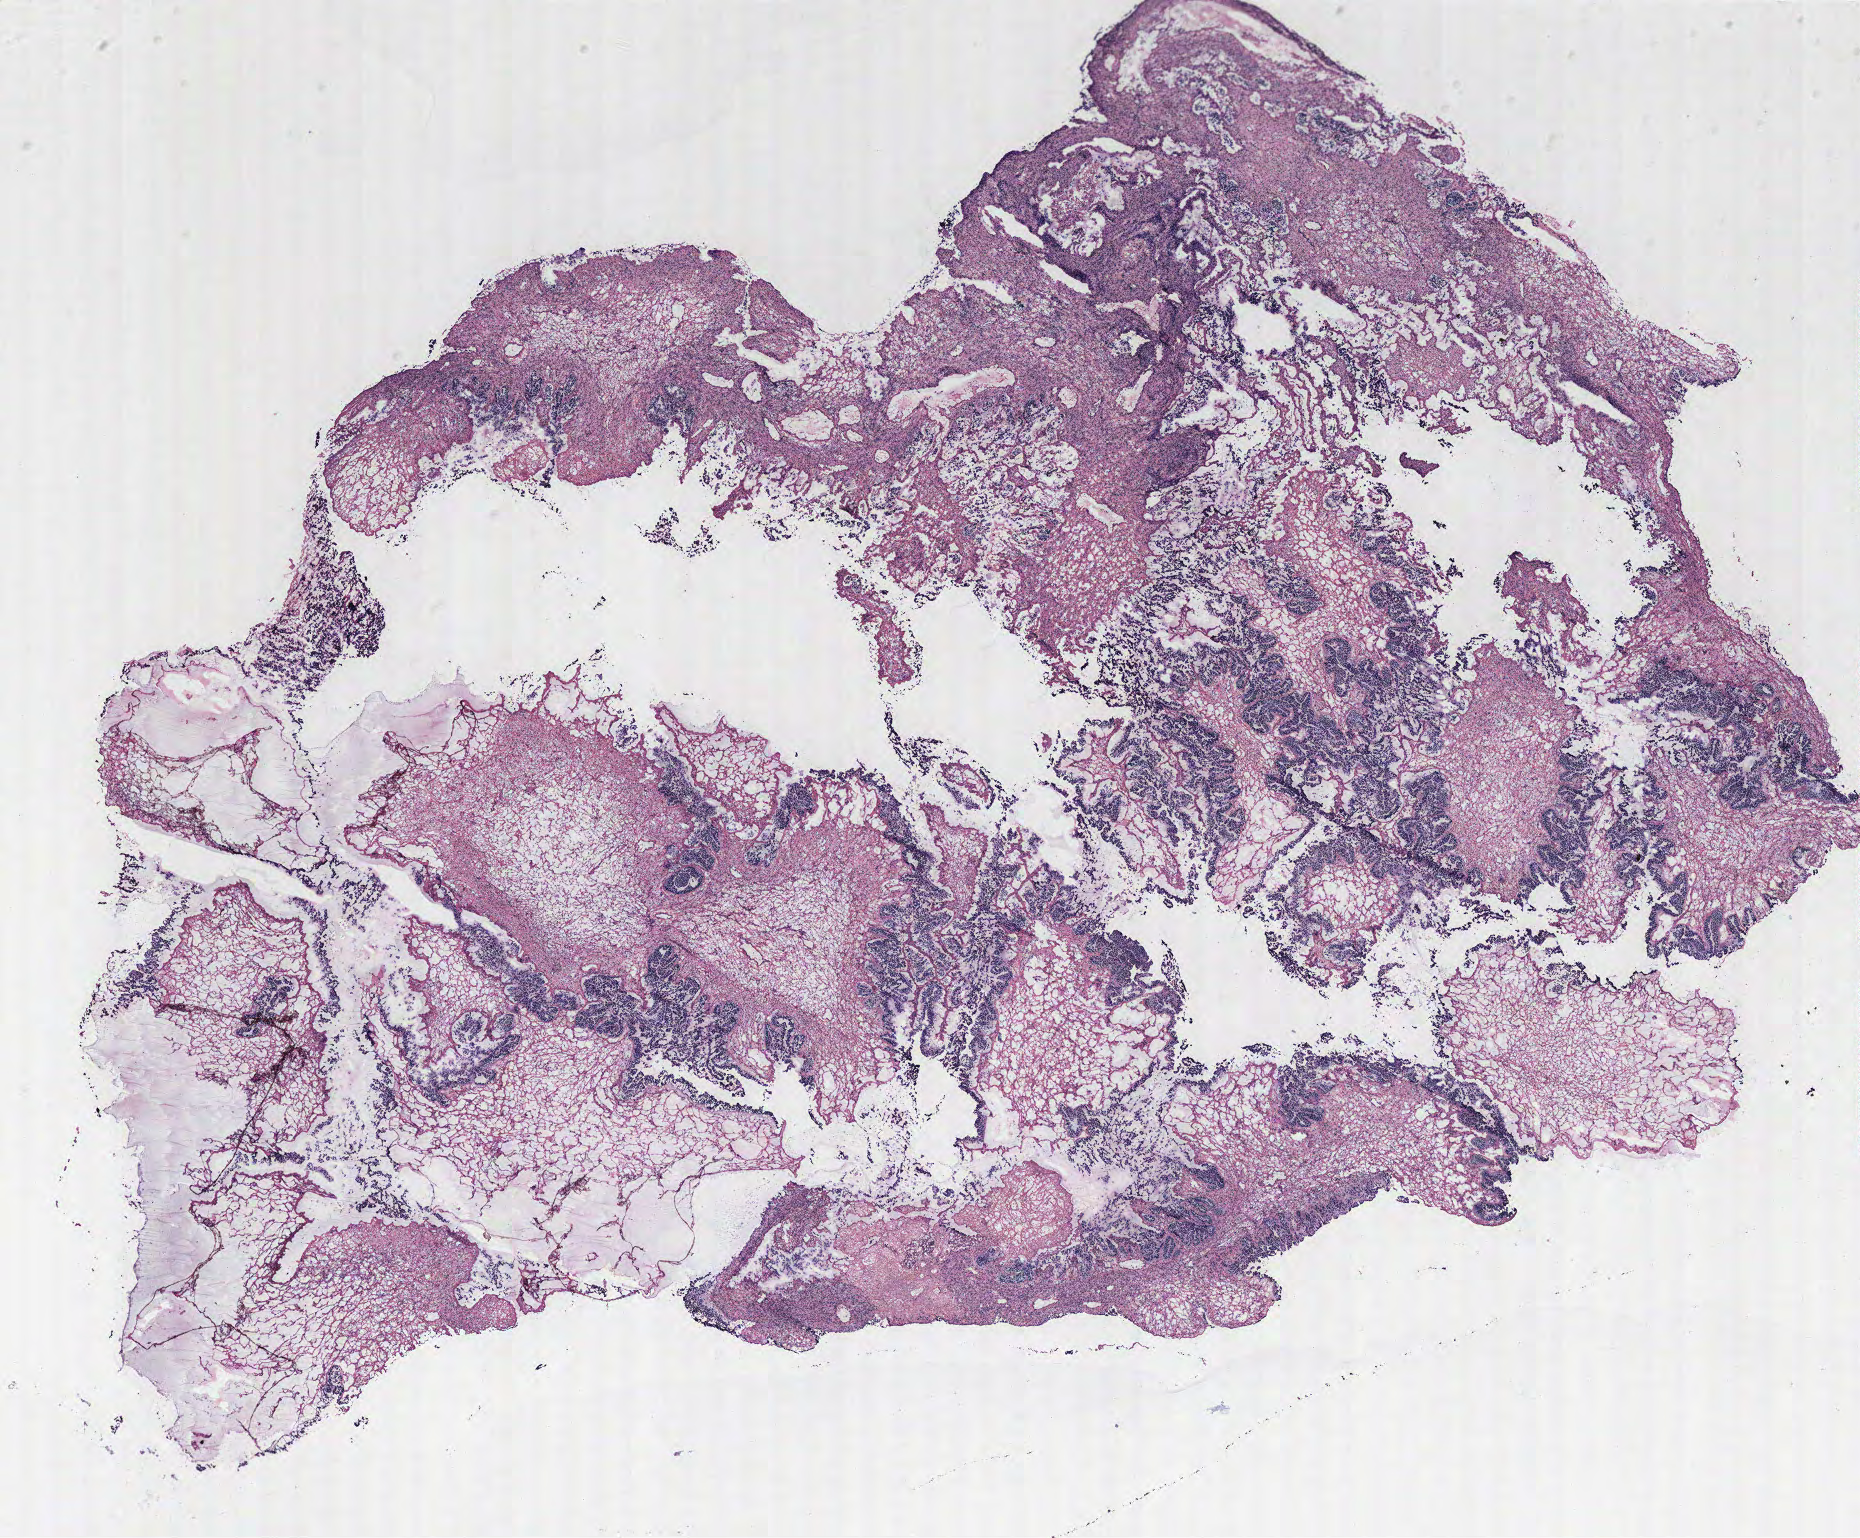
Whole-slide histology image, H&E-stained — whole scanned area (about 14.9 x 12.3 mm) shown as a low-resolution overview; ovary, tumour tissue. 79-year-old female patient.
Histologic diagnosis: Serous adenocarcinoma, NOS. Primary tumour site (as recorded): ovary.